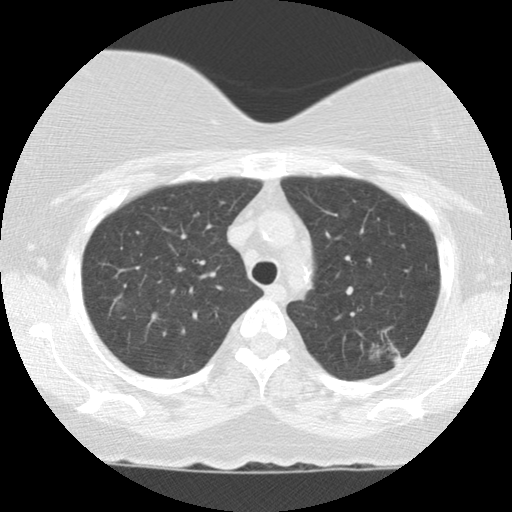
Low-dose screening chest CT, axial slice. Baseline annual screen. Lung window (W 1500 / L -600 HU). 2.5 mm slice thickness. 512 × 512 image matrix, field of view 310 × 310 mm. Female participant, aged 56 years at enrolment.
Expert reader's lesion annotation, bounding box (x1, y1, x2, y2) in pixels: (357, 318, 419, 383). The screening reader recorded 4 non-calcified nodules or masses ≥4 mm on this exam (left upper lobe, left upper lobe, right upper lobe, left upper lobe); which of them this box marks is not recorded. Official screen result: positive, change unspecified: nodule(s) >= 4 mm or enlarging nodule(s), mass(es), or other non-specific abnormalities suspicious for lung cancer. Later outcome: lung cancer diagnosed 798 days after this screen (after the third annual screen) — adenocarcinoma, NOS, left upper lobe, moderately differentiated (G2), stage IA (AJCC 6th edition), 10 mm at pathology.